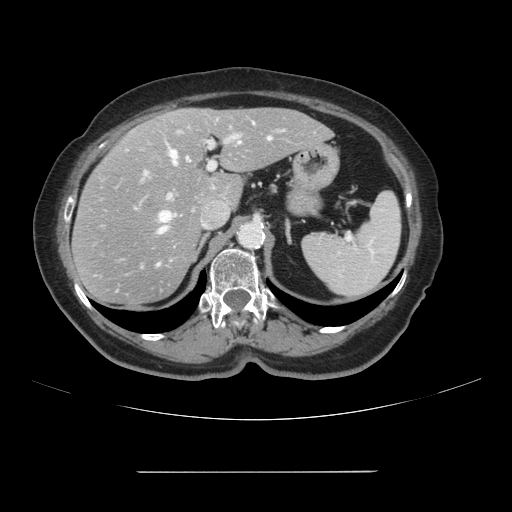
Contrast-enhanced abdominal CT, one axial slice; slice 67 of 111 in the series (ordered by position); 120 kVp; intravenous contrast given; soft-tissue window (W 400 / L 40 HU); 2.5 mm slice thickness; 512 × 512 image matrix. Female patient, age 74 years. From the clinical record (not read from this slice): diagnosis: colorectal cancer liver metastases, imaged before liver resection; multiple liver metastases: yes.
Structures marked on this image (manually delineated by an expert):
- hepatic veins: box from (x=159, y=137) to (x=272, y=233) px
- liver: (x=74, y=108)–(x=331, y=306)
- planned liver remnant (the part of the liver to remain after resection): (x=150, y=108)–(x=331, y=207)
- portal vein (with intrahepatic branches): (x=141, y=117)–(x=317, y=201)
- liver metastasis: (x=152, y=156)–(x=160, y=165)